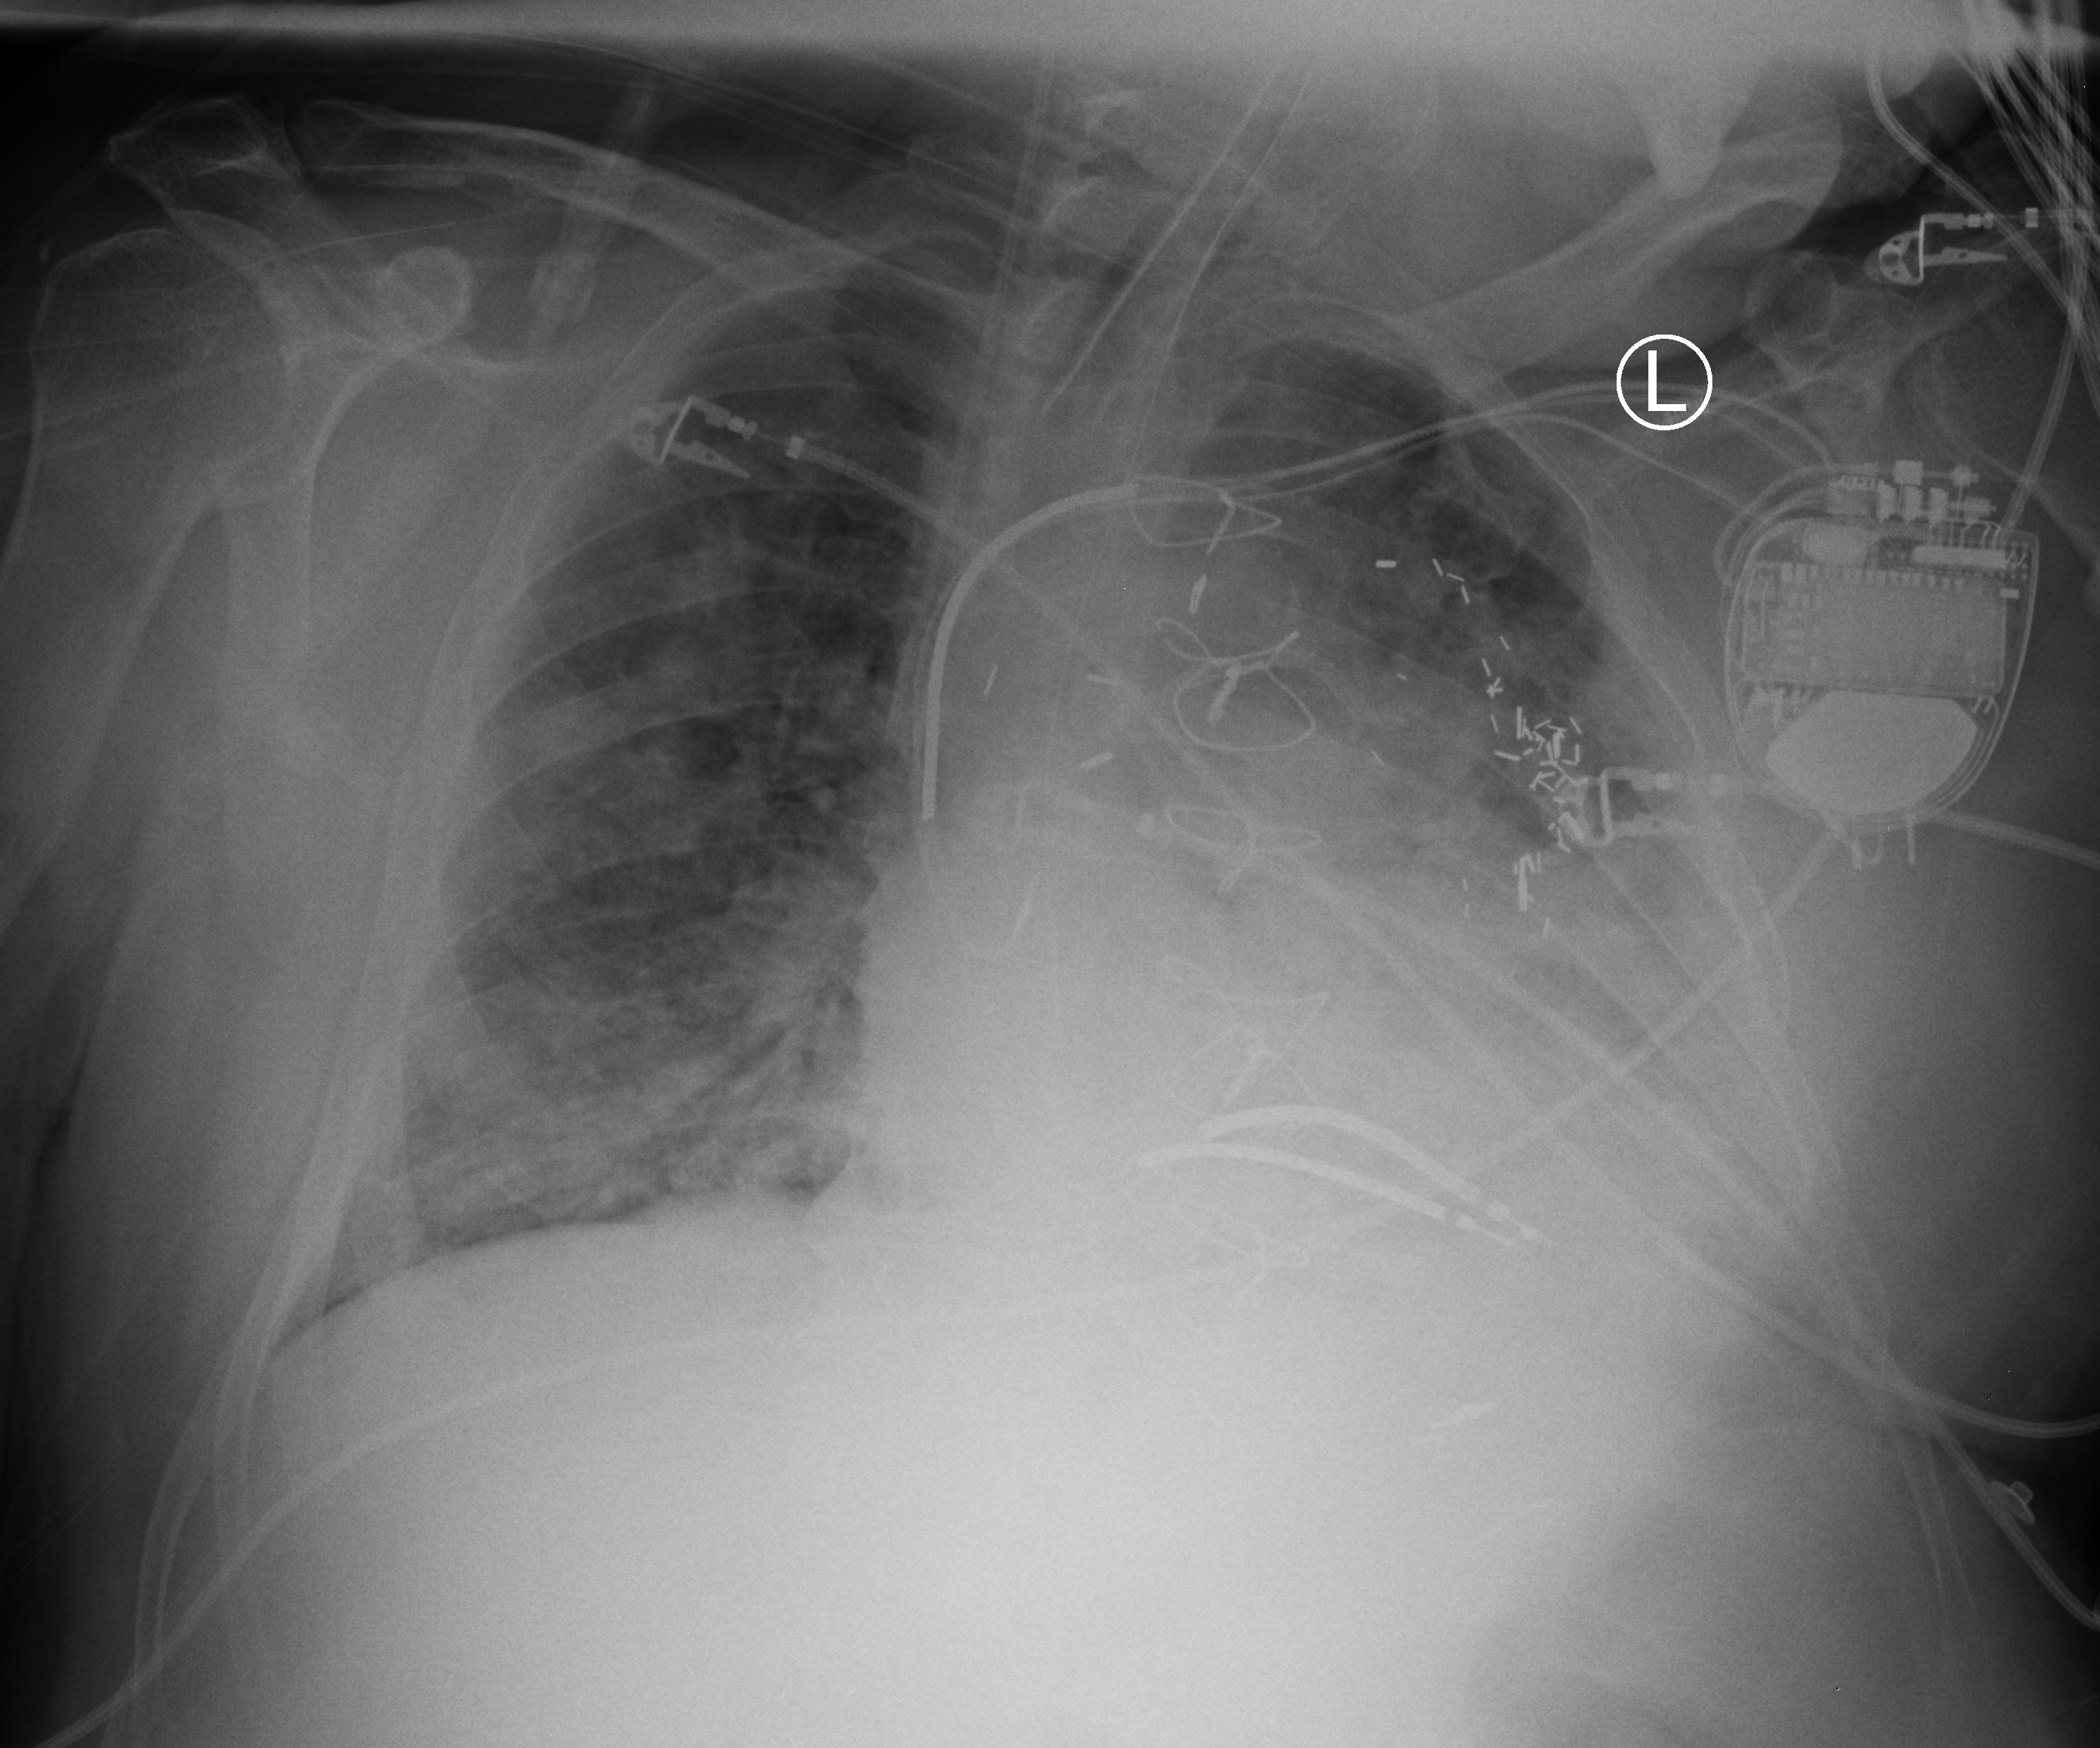
Bedside chest radiograph (computed radiography); anteroposterior (AP) projection. Patient hospitalised with COVID-19; male, aged 60–74 years.
Hospital-stay facts (about this admission, not read from this image; timing relative to this image not recorded): mechanically ventilated during this hospital stay: yes; admitted to intensive care during this hospital stay: yes; length of hospital stay: 55 days.